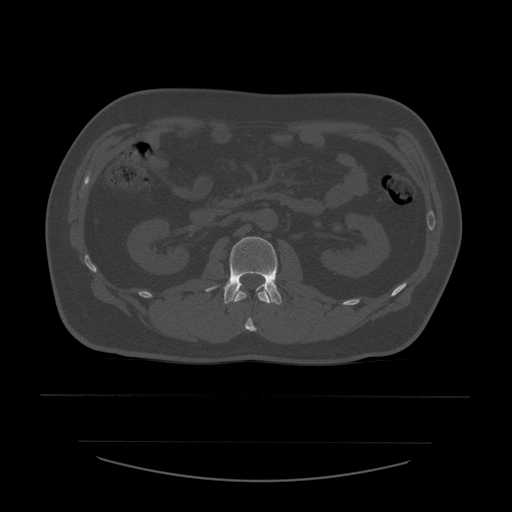
CT including the spine, one axial slice. Slice 208 of 532 in the series (ordered by position). 120 kVp. Bone window (W 1800 / L 400 HU). 1.25 mm slice thickness. 512 × 512 image matrix, field of view 441 × 441 mm. Patient age 44 years. From the clinical record (not read from this slice): primary cancer: soft tissue sarcoma.
Outlined on this slice (semi-automatically segmented with operator editing):
- L1 vertebra: box from (x=233, y=290) to (x=273, y=332) px
- L2 vertebra: (x=206, y=237)–(x=282, y=305)